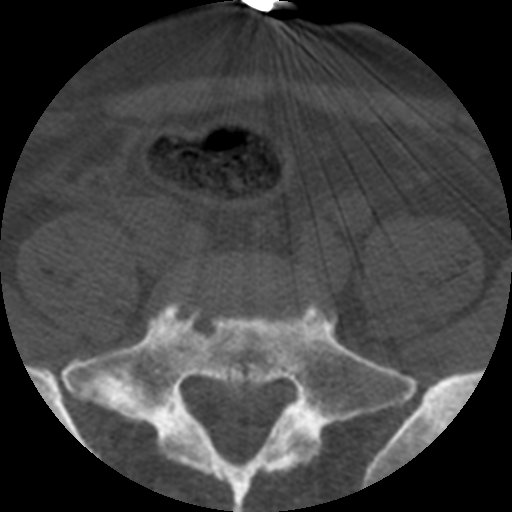
CT including the spine, one axial slice. Position 45 of 508 along the scan axis. Bone window (W 1800 / L 400 HU). 512 × 512 image matrix, field of view 160 × 160 mm. Patient age 57 years. Case-level facts recorded for this patient, not image findings: primary cancer: prostate.
Structures marked on this image (semi-automatic segmentation, software-assisted and operator-edited):
- L5 vertebra: bounding box (x1, y1, x2, y2) in pixels: (234, 256, 282, 283)